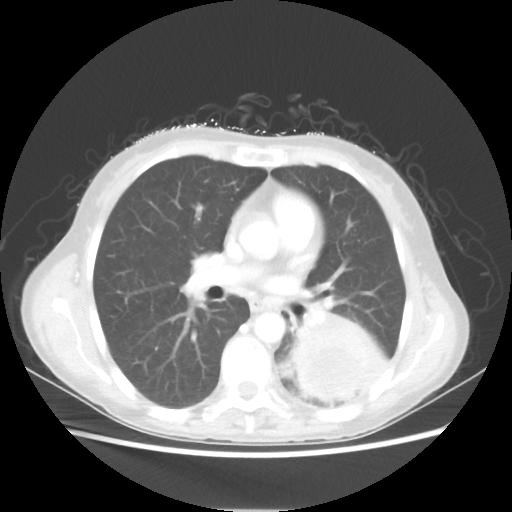
Chest CT, one axial slice; position 30 of 56 along the scan axis; lung window (W 1500 / L -600 HU); 512 × 512 image matrix, field of view 360 × 360 mm. Patient: female, 53 years. From the clinical record (not read from this slice): clinical TNM (as recorded): T3 N0 M0.
Annotated regions visible in this slice (bounding box drawn by a radiologist):
- lung tumour (recorded histology: adenocarcinoma): bounding box [x1, y1, x2, y2] px = [294, 307, 387, 401]